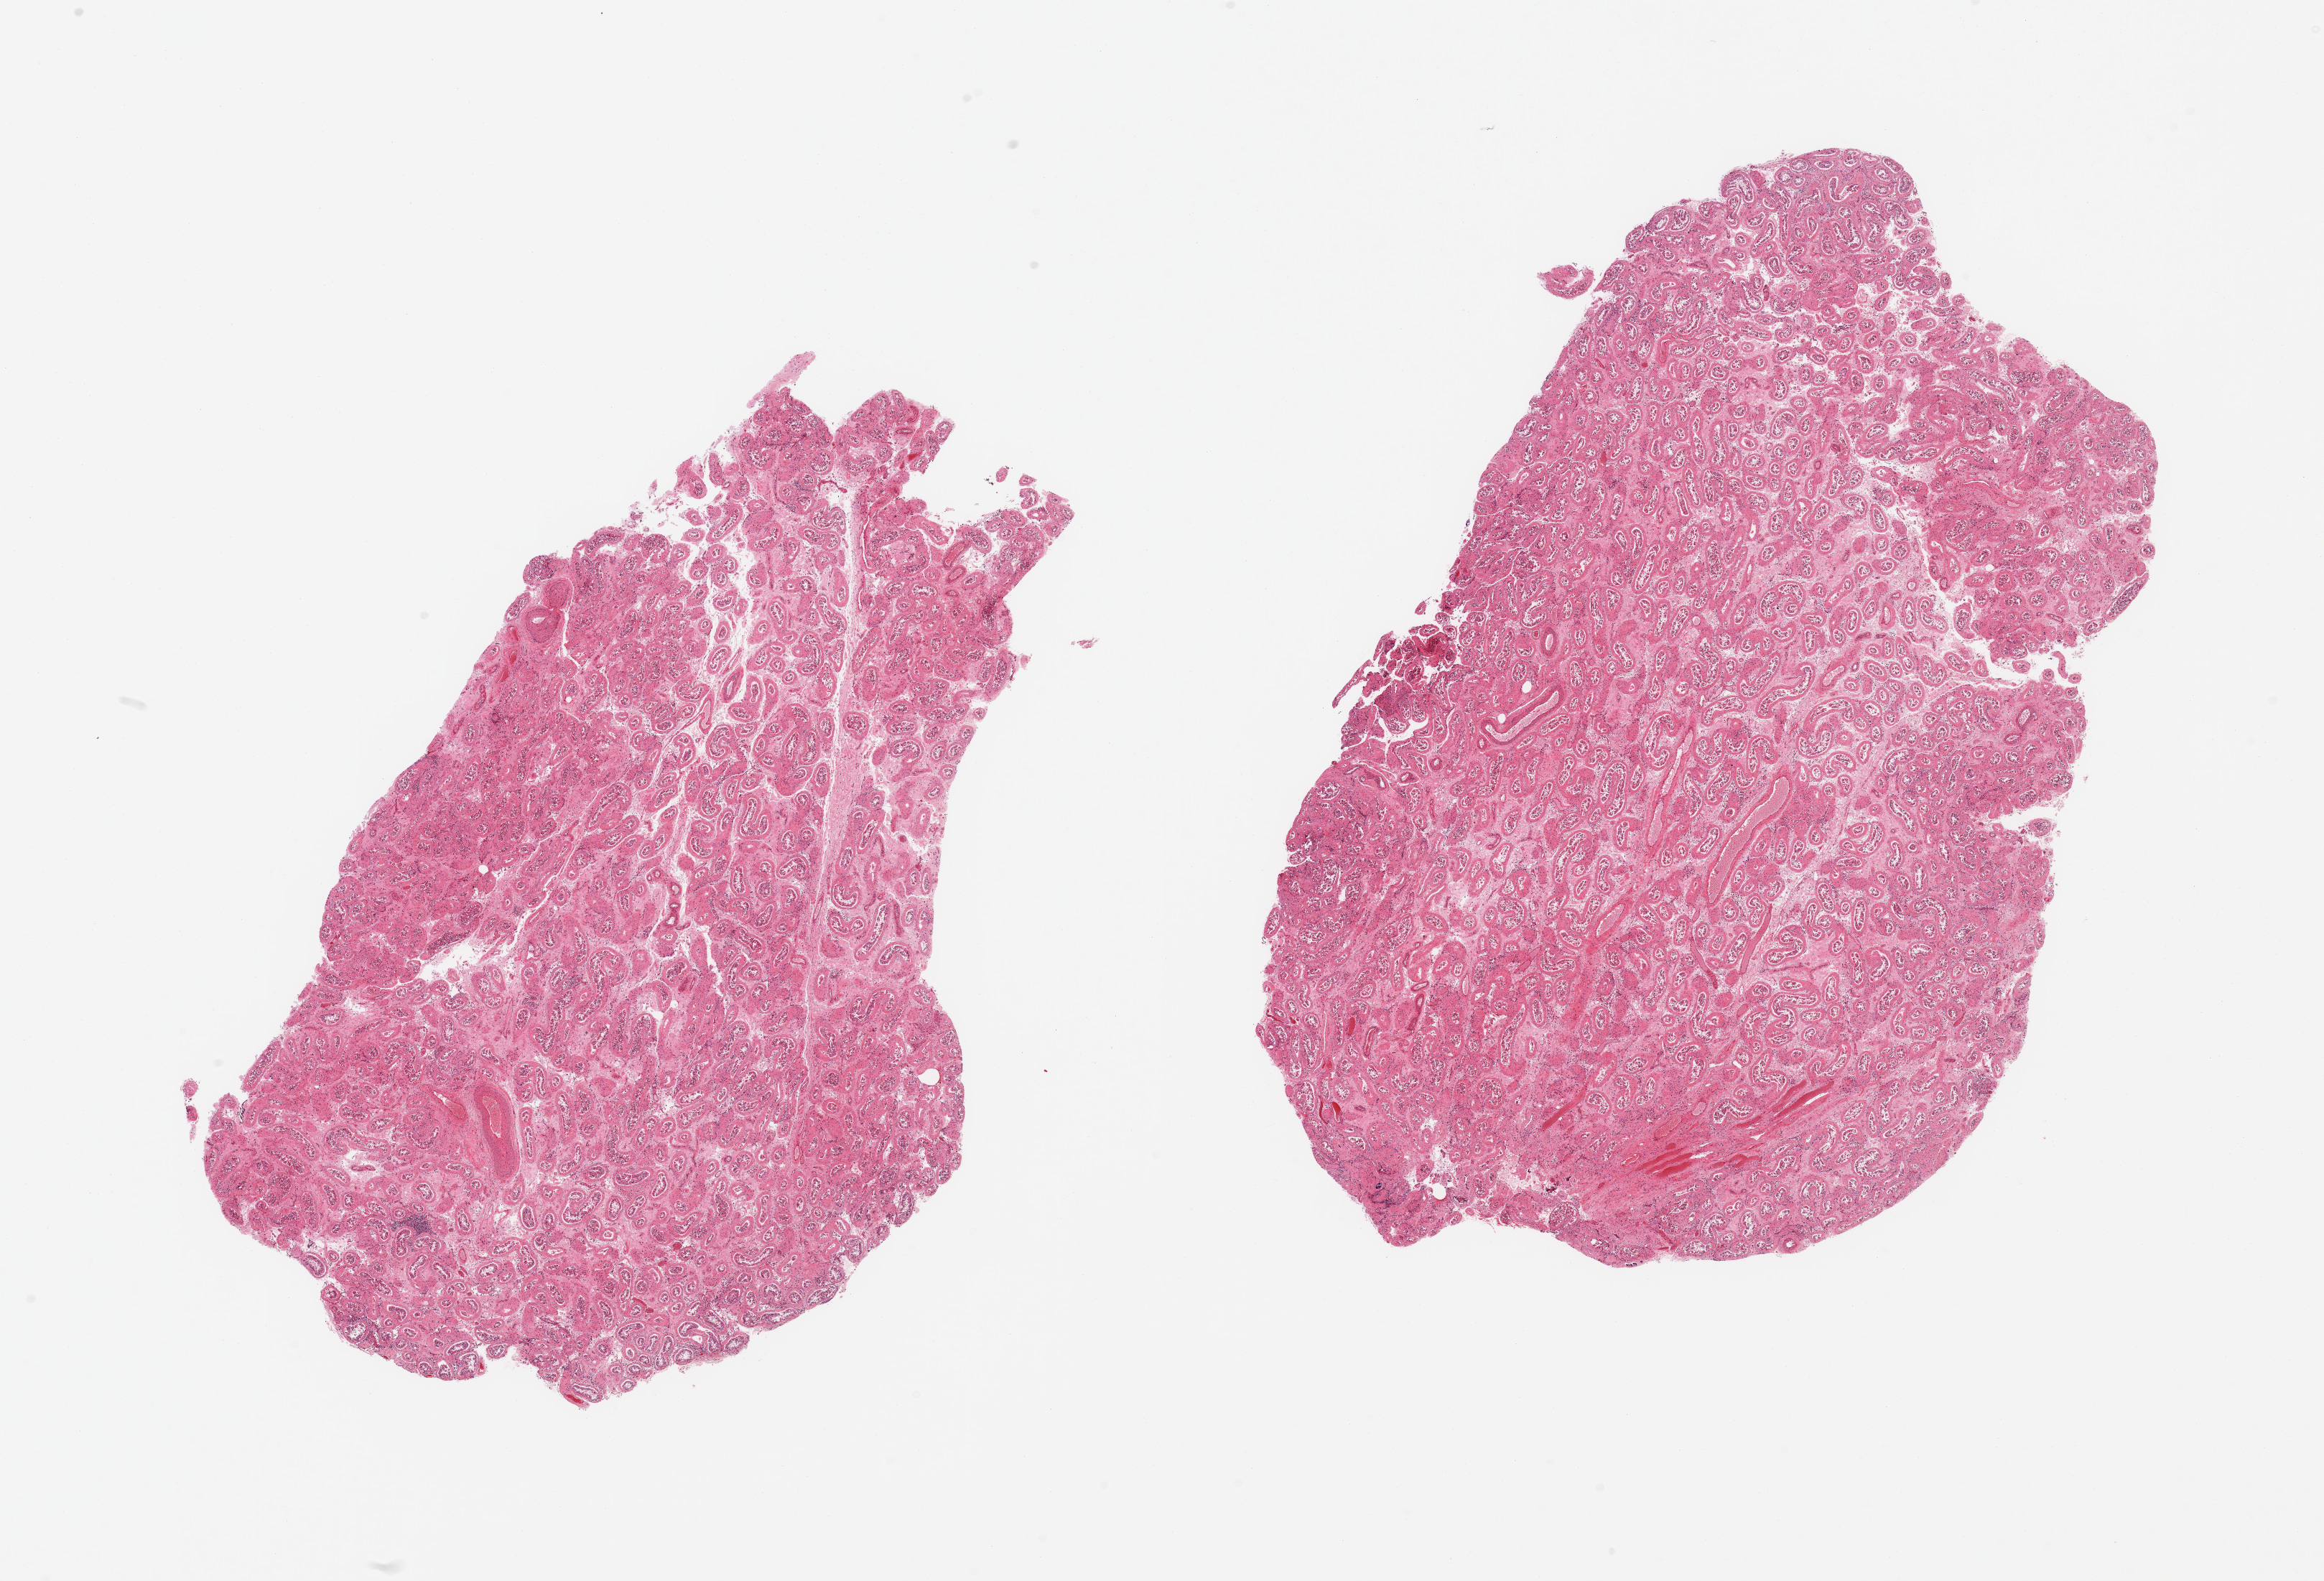
Hematoxylin and eosin (H&E) whole-slide image — whole scanned area (about 25.6 x 17.4 mm, slide scanned at 20x) shown as a low-resolution overview. PAXgene-fixed, paraffin-embedded tissue. Sampled site (target tissue): testis. Donor tissue sample. Male donor.
• pathologist's review note for this sample: 2 pieces, atrophic, spermatogenesis is rmarkedly reduced/absent